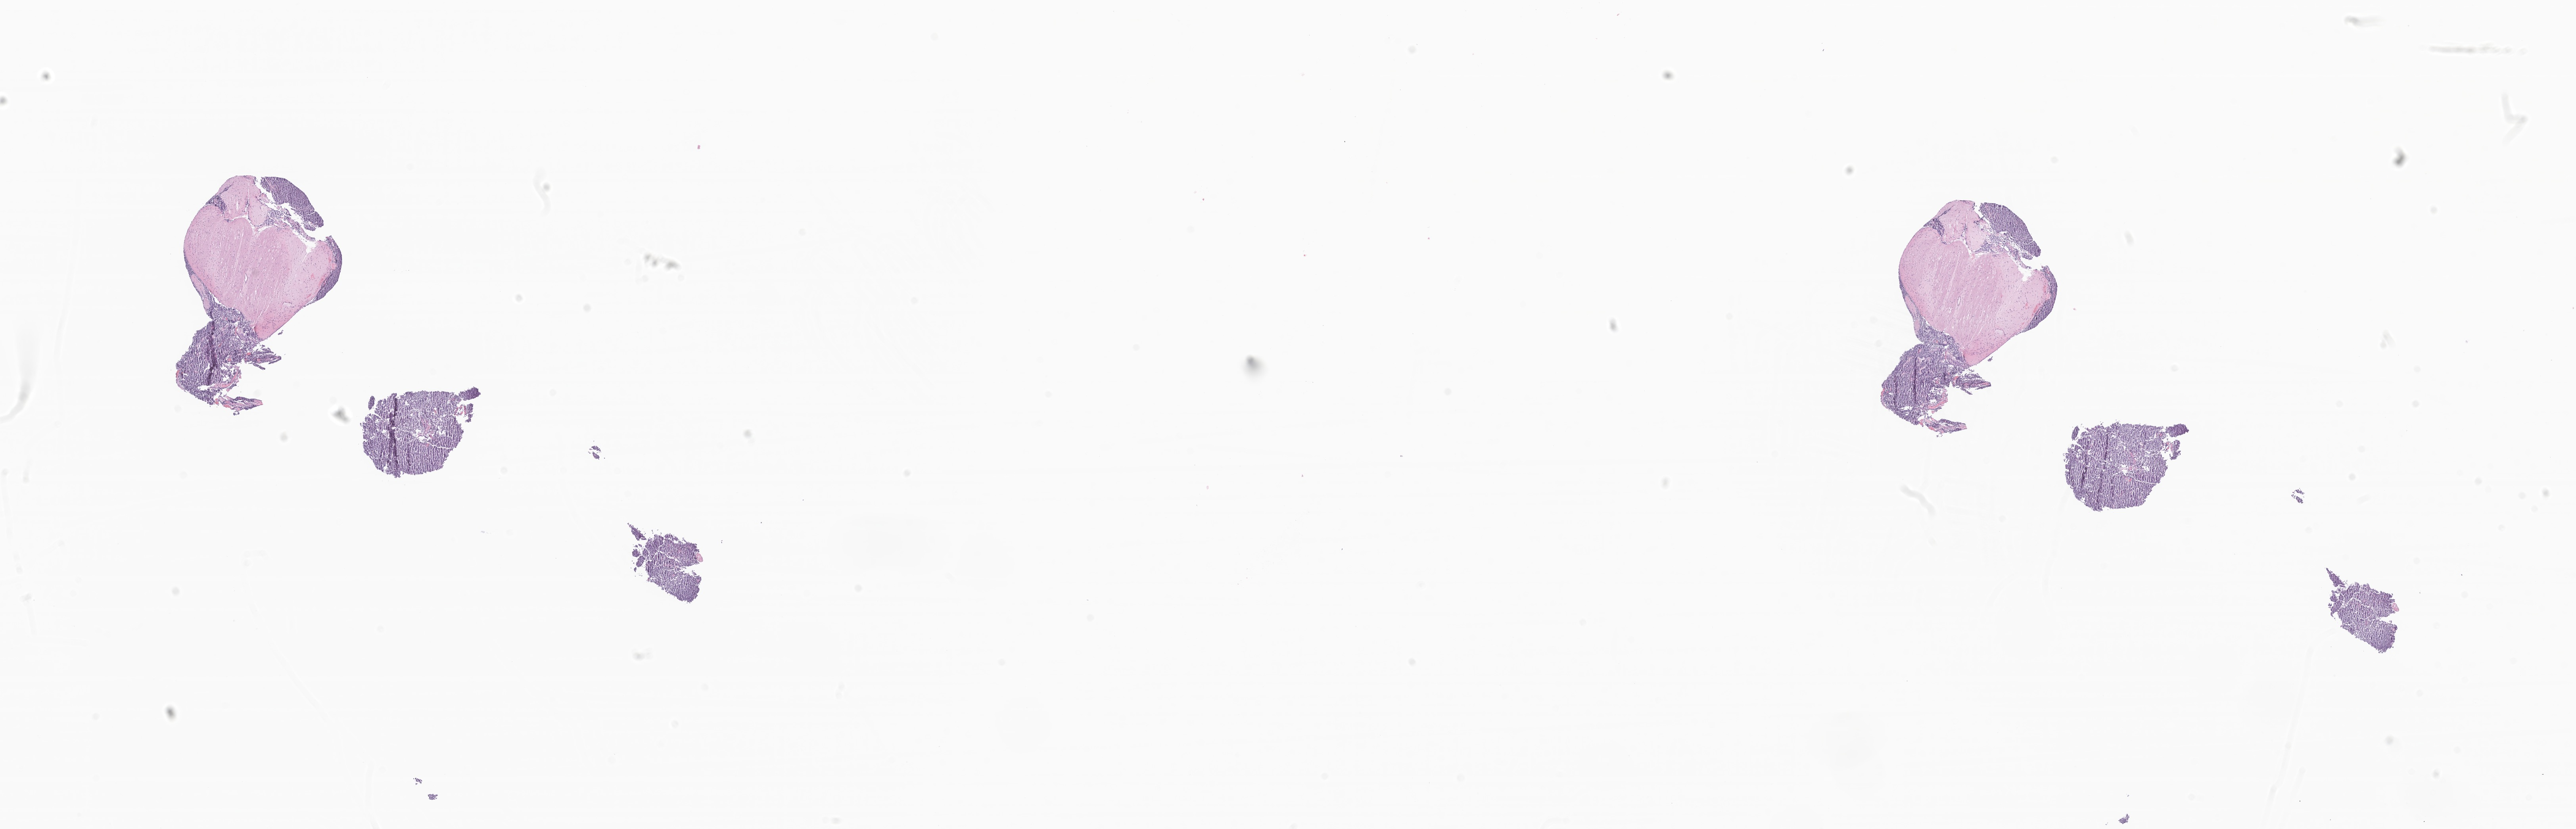
Haematoxylin and eosin whole-slide image of tumor tissue from the pineal gland, low-resolution overview of the scanned area, about 27.4 x 8.8 mm; FFPE section. Patient female; age 58 months (4 years 10 months).
Recorded diagnosis: Neoplasm, uncertain whether benign or malignant.